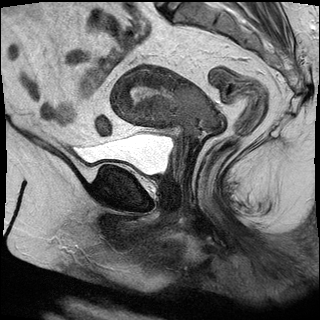
Pelvic MRI for cervical cancer, one sagittal slice; T2-weighted; 1.5 T; TE 89 ms, TR 2930 ms; 4 mm slice thickness; 320 × 320 image matrix, field of view 260 × 260 mm. Female patient, age 53 years.
Annotated regions visible in this slice (expert manual segmentation):
- uterus and cervix: bounding box (x1, y1, x2, y2) in pixels: (111, 65, 221, 144)